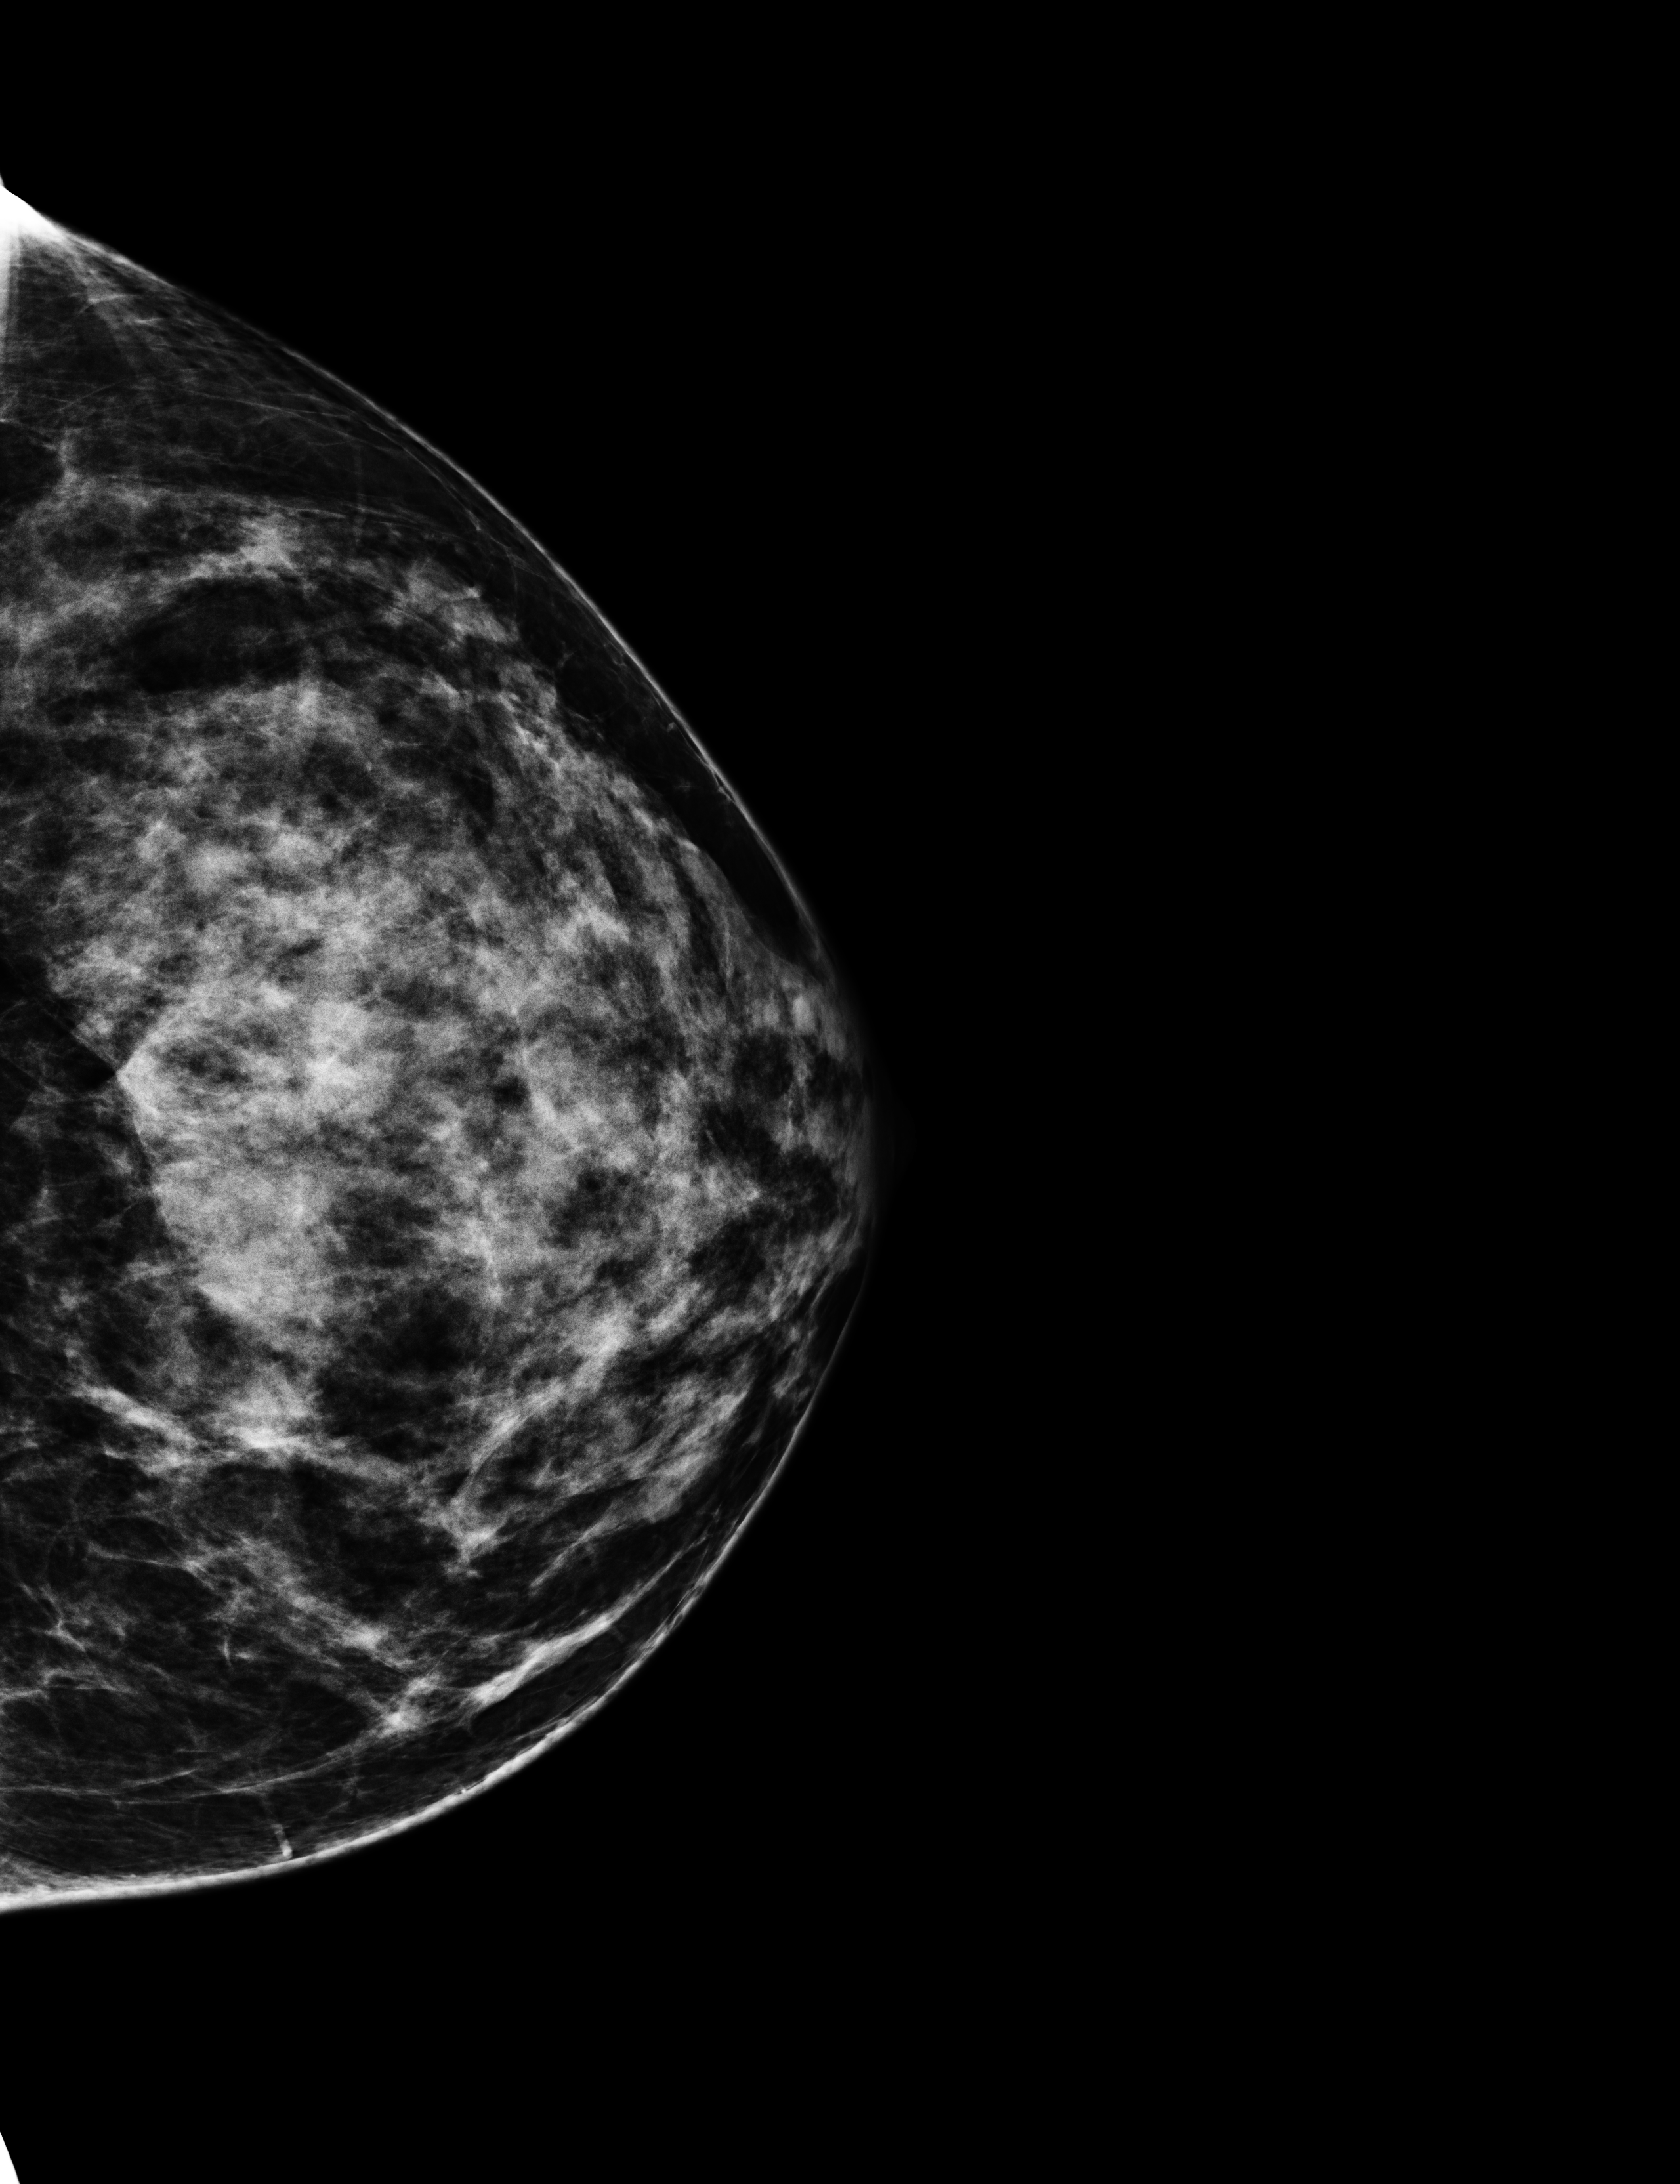
Full-field digital mammogram (FFDM), left breast, CC view, annual screening mammography examination, compressed breast thickness 53 mm. Patient aged 42 years (female).
- breast density at the screening exam (both breasts): extremely dense (BI-RADS density category d)
- final BI-RADS assessment for this screening round (tomosynthesis exam, both breasts): category 1
- recall: no recall after this screen